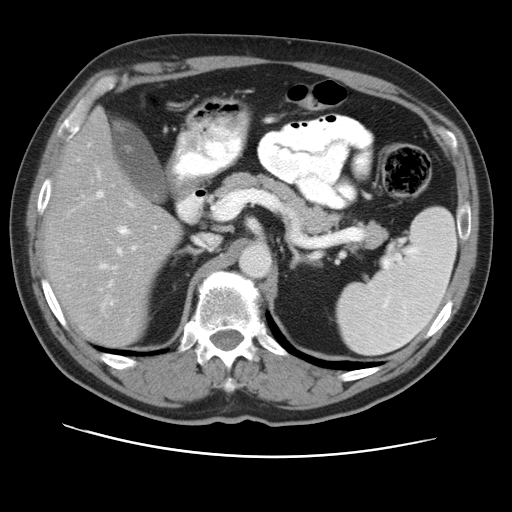
Contrast-enhanced abdominal CT, one axial slice; position 27 of 49 along the scan axis; 120 kVp; intravenous contrast given; soft-tissue window (W 400 / L 40 HU); 5 mm slice thickness; 512 × 512 image matrix, field of view 374 × 374 mm. Male patient, age 59 years. From the clinical record (not read from this slice): diagnosis: colorectal cancer liver metastases, imaged before liver resection; multiple liver metastases: yes; largest metastasis: 6.3 cm; disease in both lobes: yes.
Annotated regions visible in this slice (expert manual segmentation):
- hepatic veins: bounding box <97,191,217,249> (left, top, right, bottom; pixels)
- liver: <47,114,180,348>
- planned liver remnant (the part of the liver to remain after resection): <49,114,180,348>
- portal vein (with intrahepatic branches): <98,172,136,304>